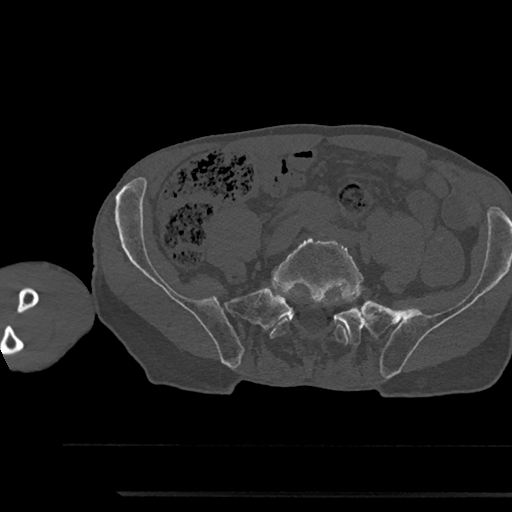
CT including the spine, one axial slice; position 320 of 797 along the scan axis; 120 kVp; bone window (W 1800 / L 400 HU); 0.5 mm slice thickness; 512 × 512 image matrix. Patient: male, 79 years. Case-level facts recorded for this patient, not image findings: primary cancer: prostate.
Outlined on this slice (semi-automatically segmented with operator editing):
- L5 vertebra: box from (x=269, y=234) to (x=362, y=344) px